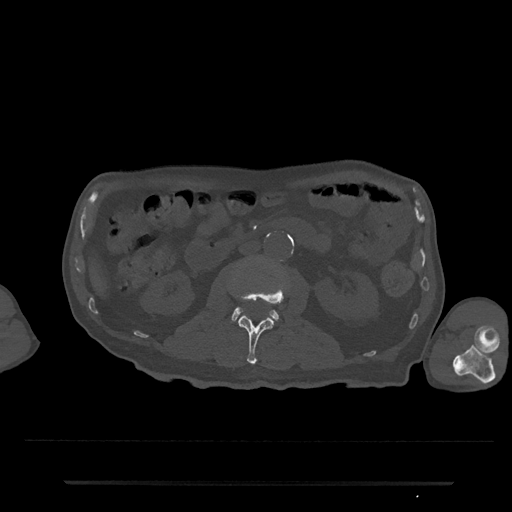
CT including the spine, one axial slice. Slice 35 of 797 in the series (ordered by position). Reconstruction kernel Br40s/3. Bone window (W 1800 / L 400 HU). 0.5 mm slice thickness. 512 × 512 image matrix, field of view 427 × 427 mm. Patient: male, 74 years. From the clinical record (not read from this slice): primary cancer: prostate.
Structures marked on this image (semi-automatic segmentation, software-assisted and operator-edited):
- L2 vertebra: bounding box <233,283,285,365> (left, top, right, bottom; pixels)
- L3 vertebra: <231,306,279,322>